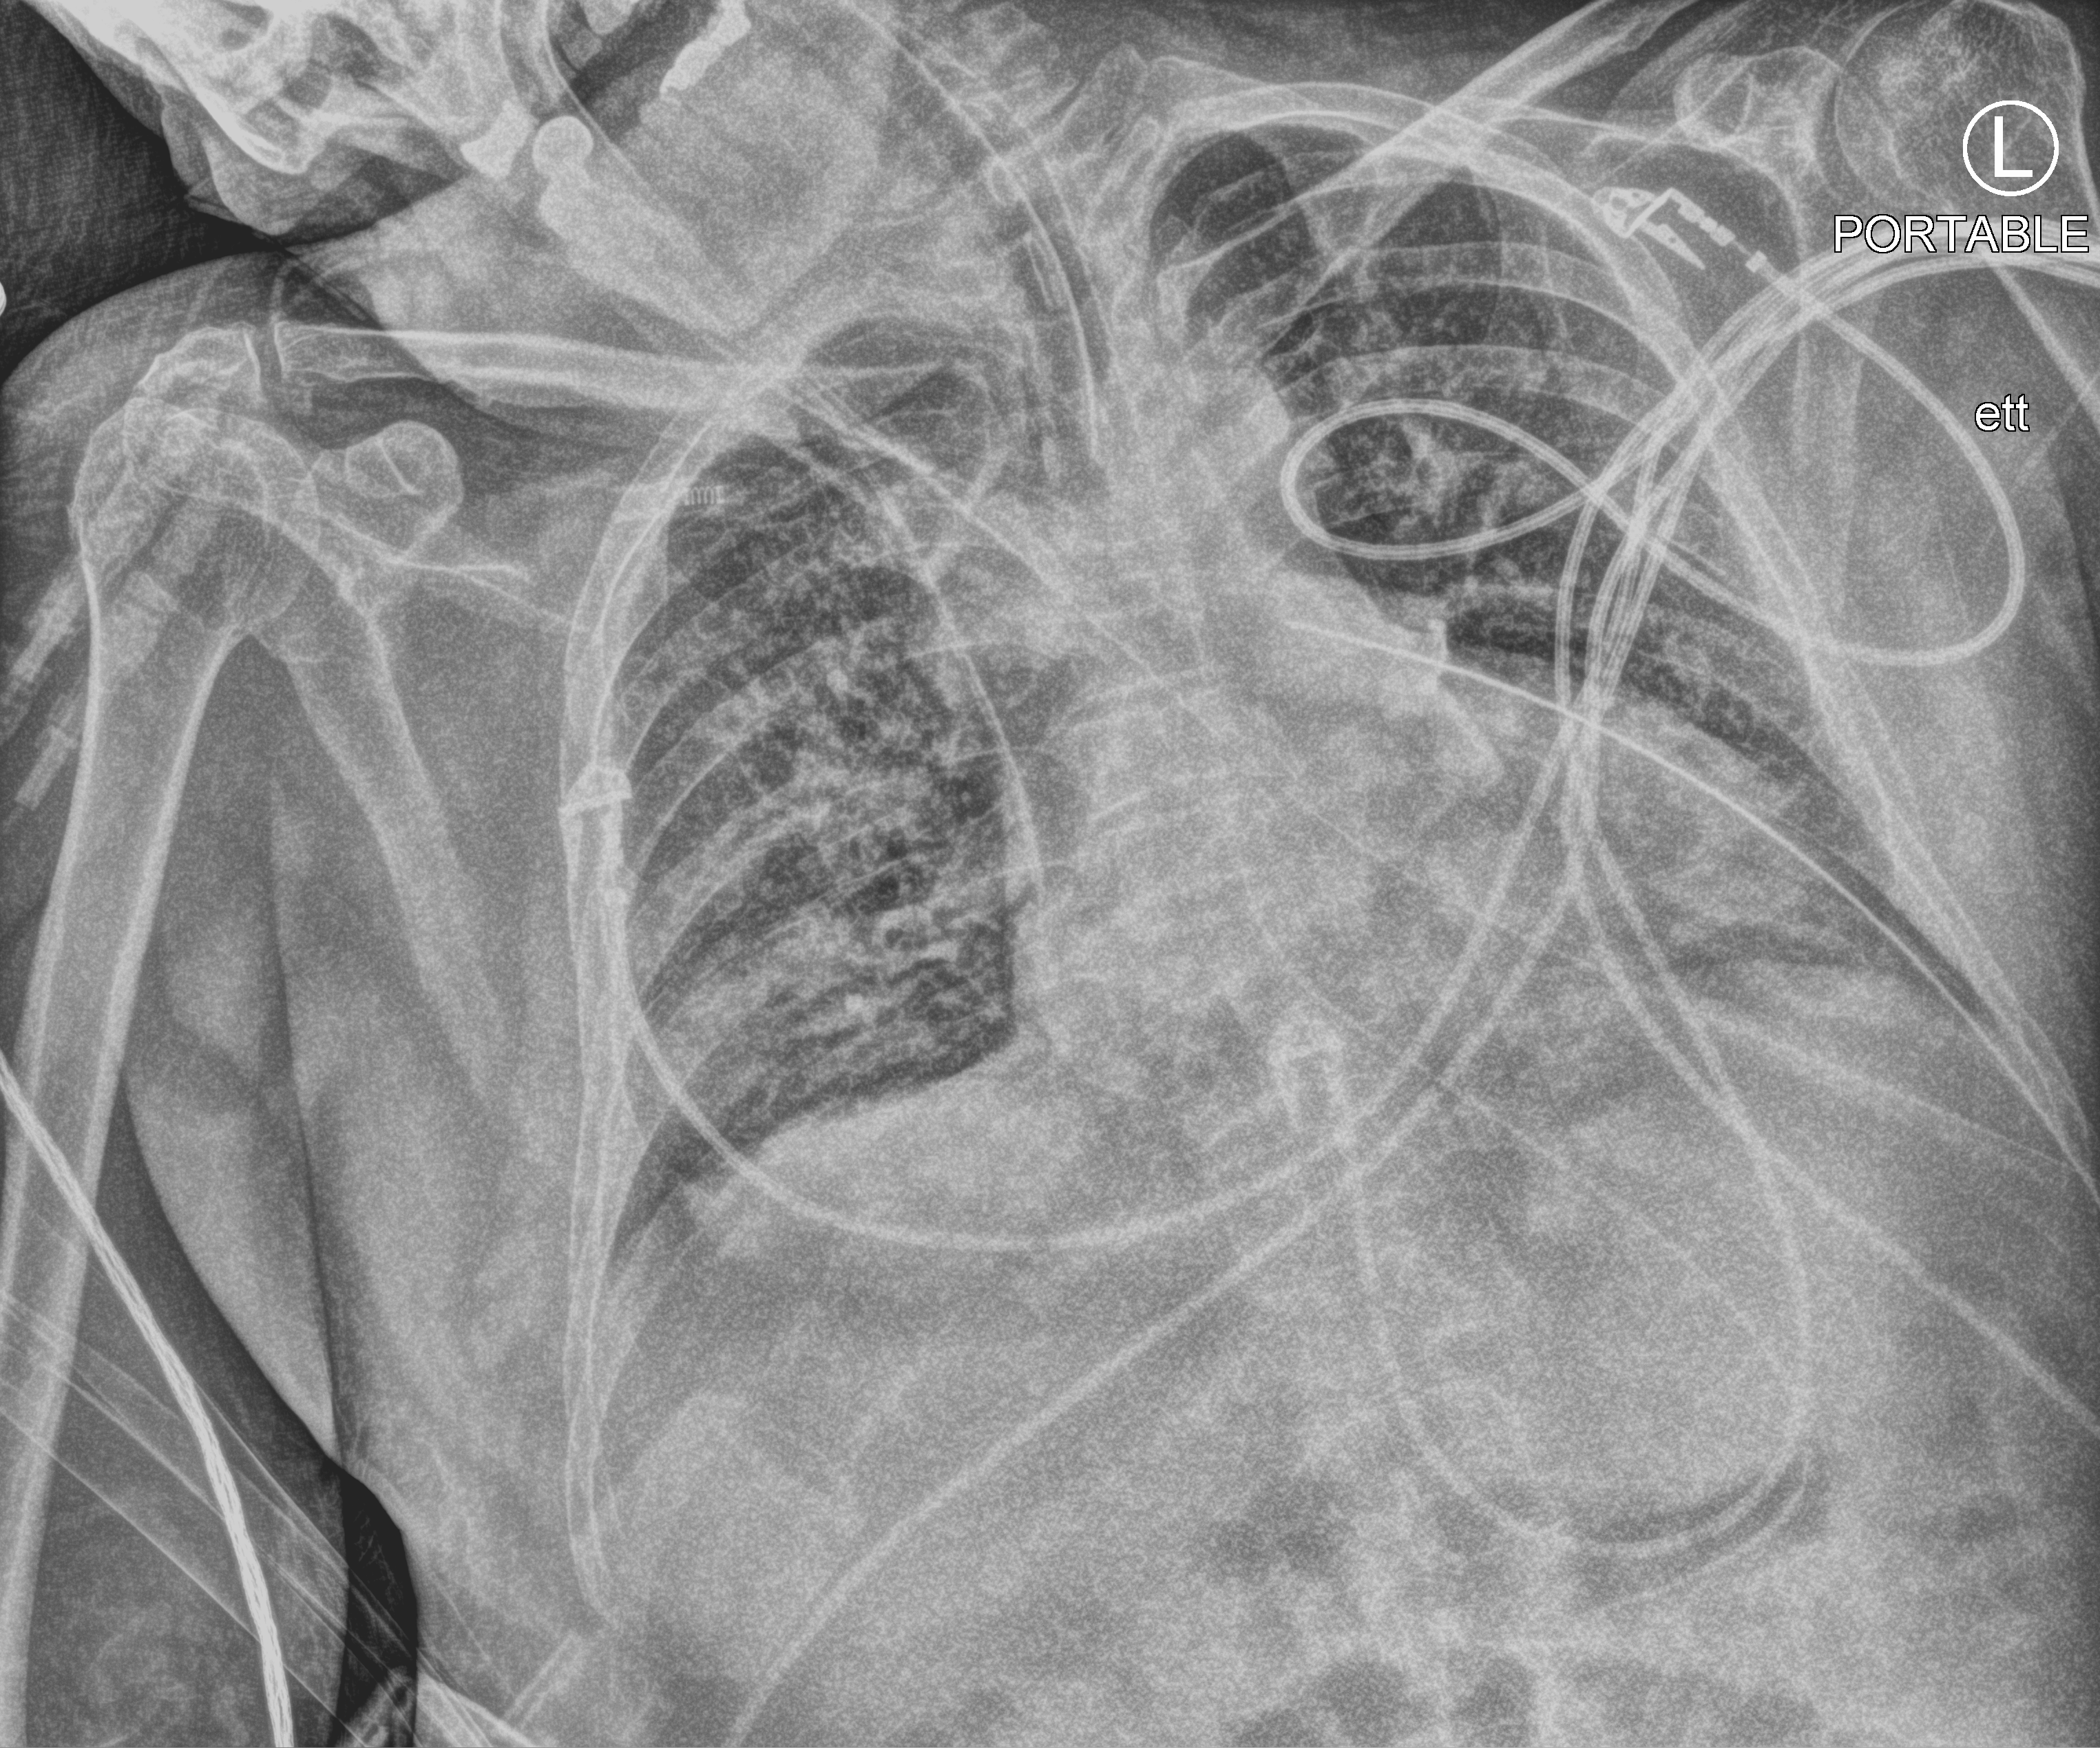
Portable chest radiograph; anteroposterior (AP) projection. Patient hospitalised with COVID-19; male, aged 60–74 years.
Admission-level facts for this patient (not findings on this image; timing relative to this image not recorded): admitted to intensive care during this hospital stay: yes.